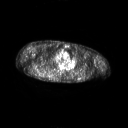
FDG PET of an extremity soft-tissue mass (from a PET/CT study), one axial slice; position 180 of 267 along the scan axis; 3.27 mm slice thickness; 128 × 128 image matrix. Patient: male, 61 years. Case-level facts recorded for this patient, not image findings: histological type: pleiomorphic spindle cell undifferentiated; grade: high; site of the primary tumour: right parascapusular.
Annotated regions visible in this slice (expert contour drawn on MRI and transferred to this co-registered scan by the dataset authors):
- gross tumour volume including surrounding oedema: bounding box (x1, y1, x2, y2) in pixels: (34, 70, 58, 78)
- gross tumour volume (mass): (39, 70, 47, 77)